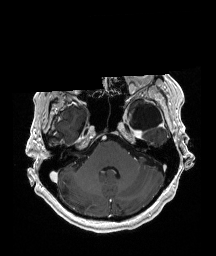
Brain MRI from a brain-tumour surgery series, one axial slice. T1-weighted post-contrast. 1 mm slice thickness. 216 × 256 image matrix, field of view 211 × 250 mm. Case-level facts recorded for this patient, not image findings: histopathology: Glioblastoma; WHO grade: 4; IDH mutation: no; tumour location: Left Temporal.
Structures marked on this image (expert manual segmentation):
- previous resection cavity: bounding box <131,104,162,130> (left, top, right, bottom; pixels)